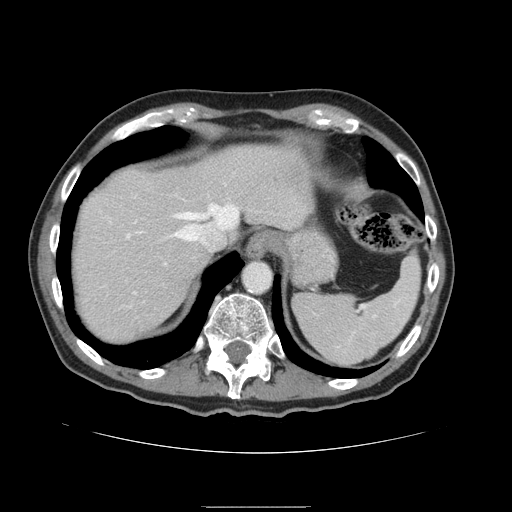
Contrast-enhanced abdominal CT, one axial slice. Position 125 of 168 along the scan axis. 120 kVp. Soft-tissue window (W 400 / L 40 HU). 2.5 mm slice thickness. 512 × 512 image matrix, field of view 386 × 386 mm. Male patient, age 74 years. From the clinical record (not read from this slice): diagnosis: colorectal cancer liver metastases, imaged before liver resection; multiple liver metastases: no; largest metastasis: 14.5 cm; disease in both lobes: yes.
Outlined on this slice (outlined manually by an expert reader):
- hepatic veins: bounding box [x1, y1, x2, y2] px = [171, 204, 239, 245]
- liver: [71, 145, 313, 345]
- planned liver remnant (the part of the liver to remain after resection): [71, 144, 313, 345]